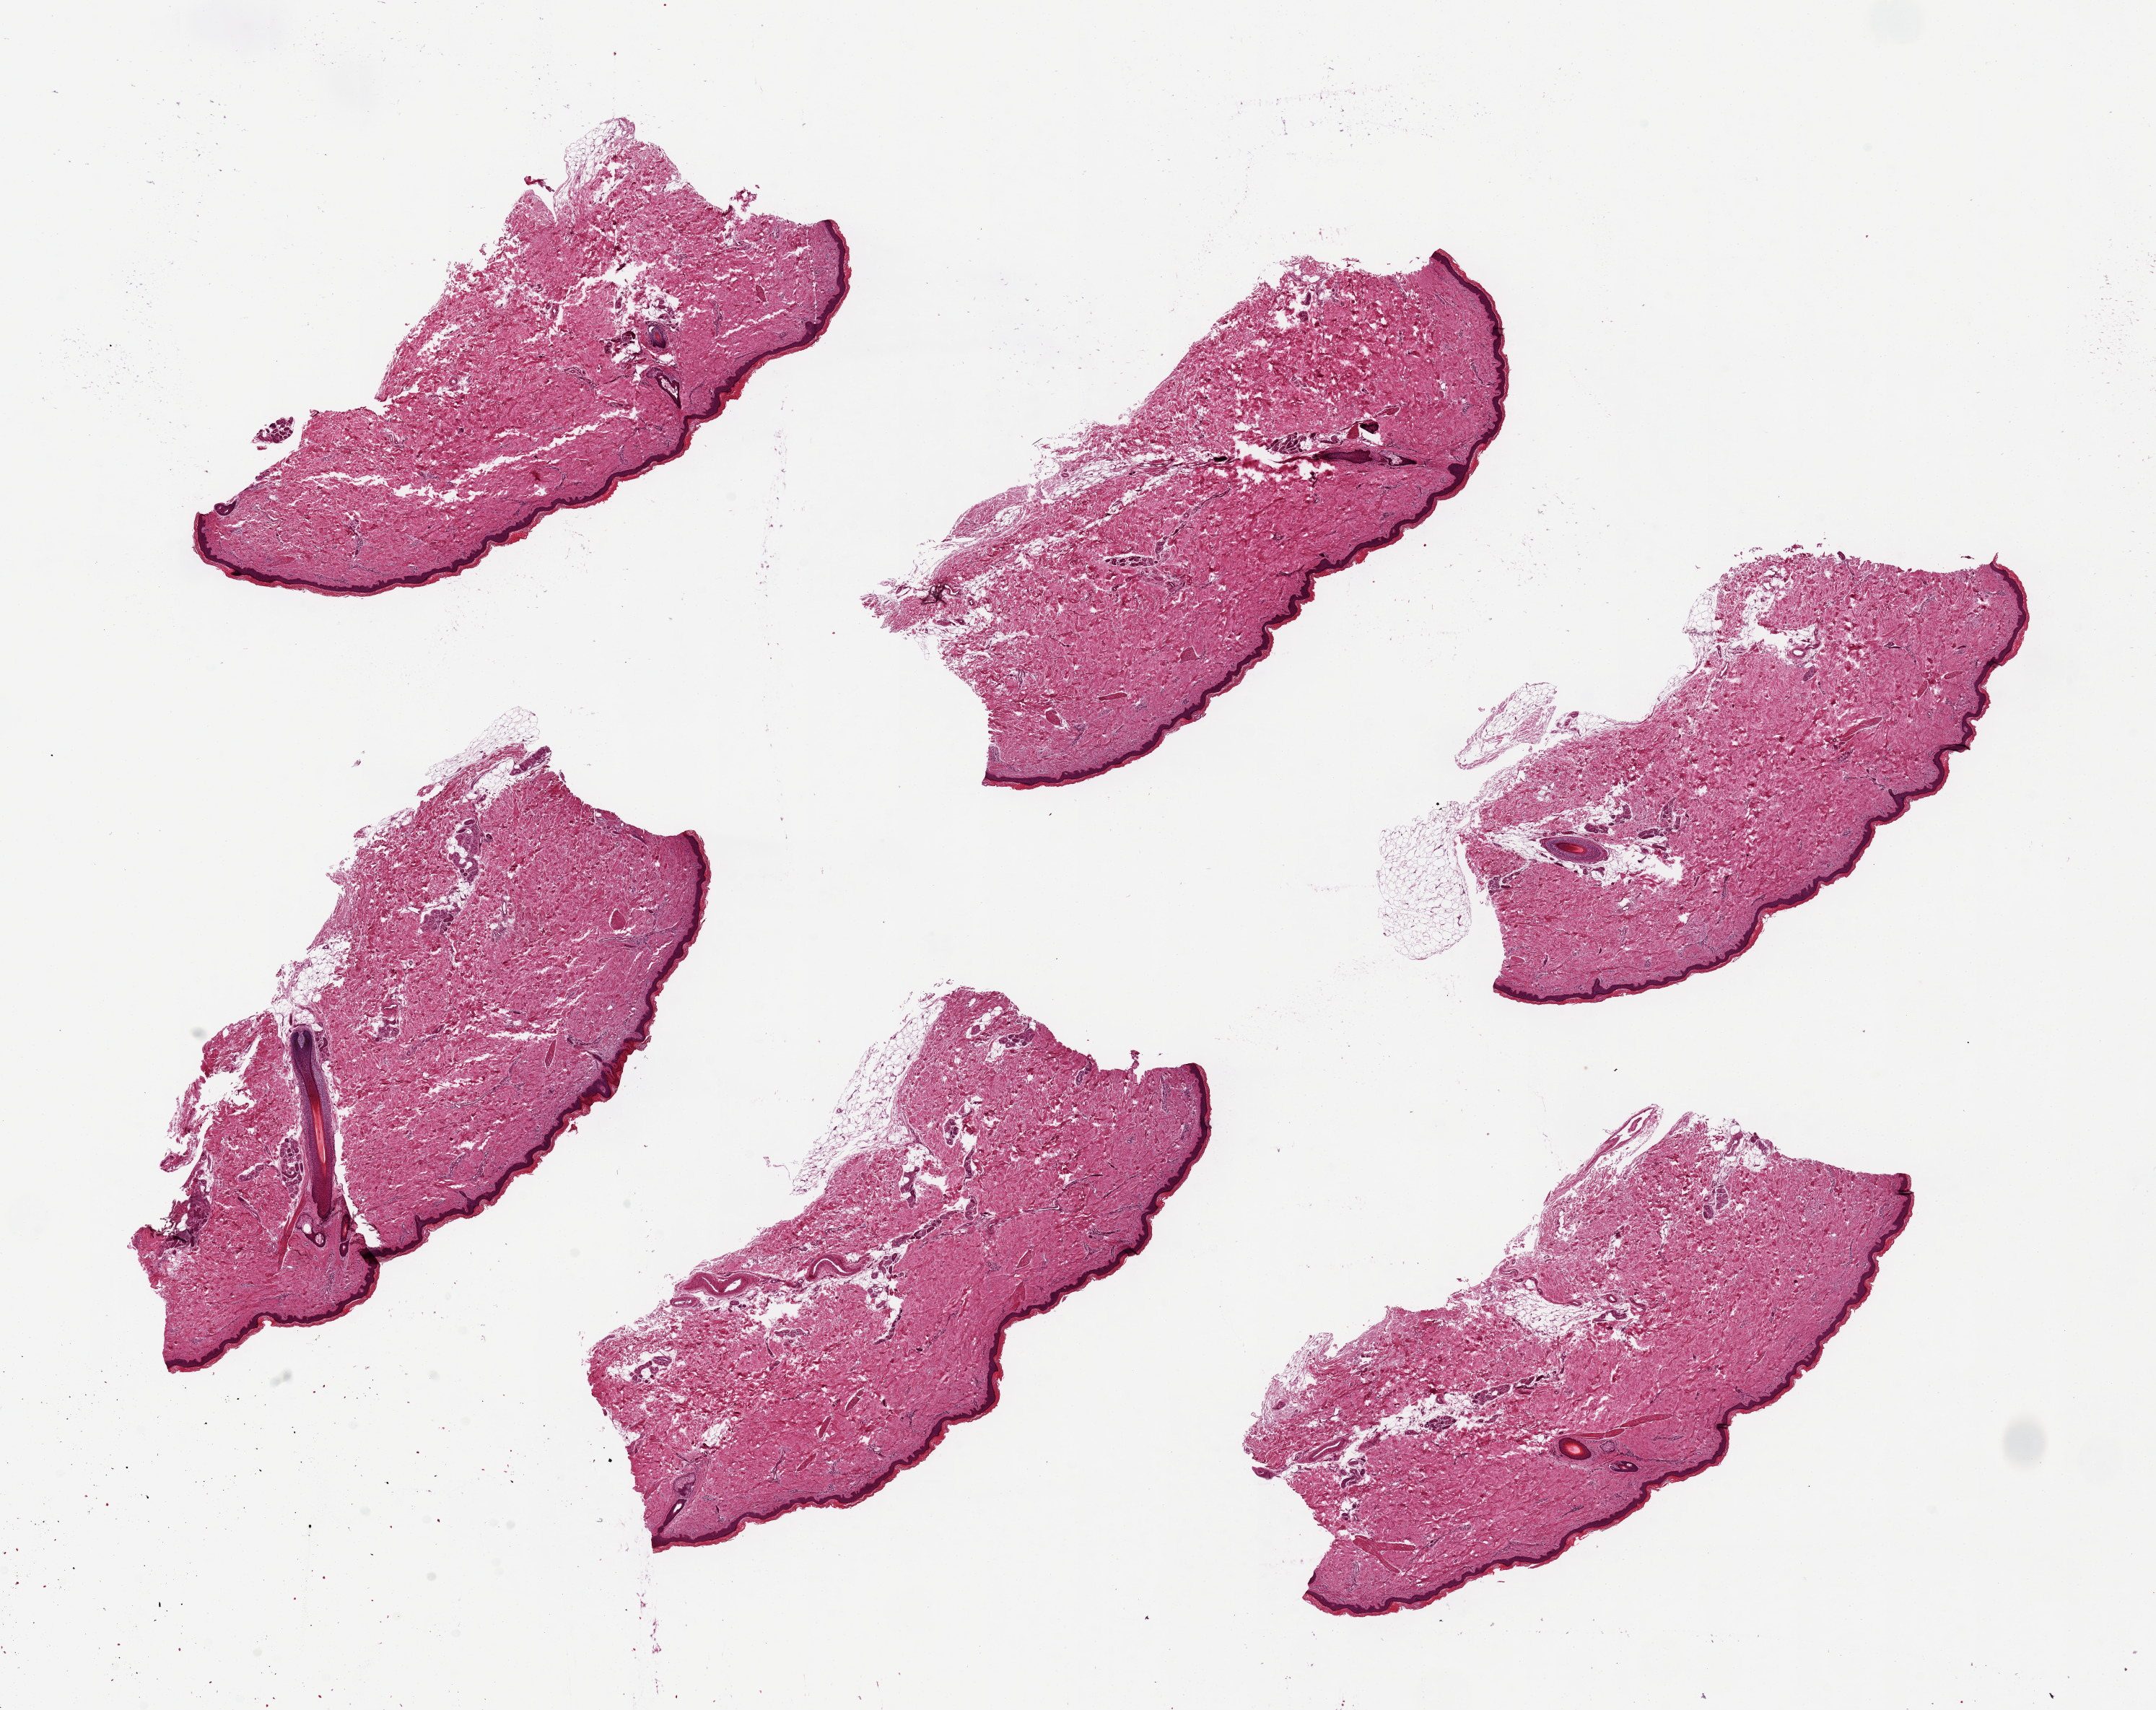
Whole-slide image, haematoxylin and eosin stain, a low-resolution overview of the entire scanned area, about 23.6 x 18.7 mm (slide scanned at 20x). PAXgene-fixed paraffin-embedded (PFPE) section. Target tissue: skin of lower leg. Donor tissue sample. Donor: male.
Pathologist's review note for this sample: 6 pieces ~7x3.5 mm, squamous epithelium is ~2-3% of thickness.